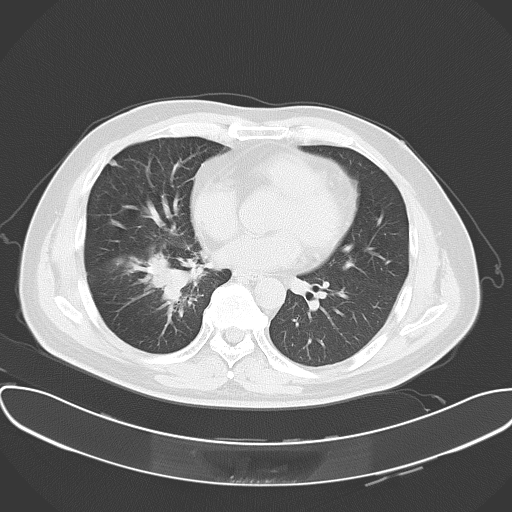
Chest CT, one axial slice; position 25 of 57 along the scan axis; reconstruction kernel B70f; 120 kVp; lung window (W 1500 / L -600 HU); 5 mm slice thickness; 512 × 512 image matrix. Male patient, age 48 years. Case-level facts recorded for this patient, not image findings: clinical TNM (as recorded): T1a N1 M1c; histopathological grade: G3.
Structures marked on this image (bounding box drawn by a radiologist):
- lung tumour (recorded histology: adenocarcinoma): bounding box (x1, y1, x2, y2) in pixels: (140, 245, 195, 306)